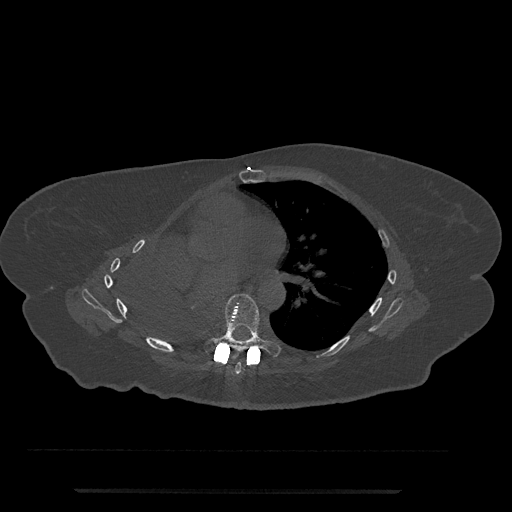
CT including the spine, one axial slice. Position 449 of 797 along the scan axis. Reconstruction kernel Br40s/3. 120 kVp. Bone window (W 1800 / L 400 HU). 0.5 mm slice thickness. 512 × 512 image matrix, field of view 440 × 440 mm. Female patient, age 51 years. From the clinical record (not read from this slice): primary cancer: neuro; vertebrae with lytic lesions (as recorded): T8.
Structures marked on this image (semi-automatic segmentation, software-assisted and operator-edited):
- T6 vertebra: bounding box [x1, y1, x2, y2] px = [235, 362, 242, 375]
- T7 vertebra: [204, 293, 281, 356]